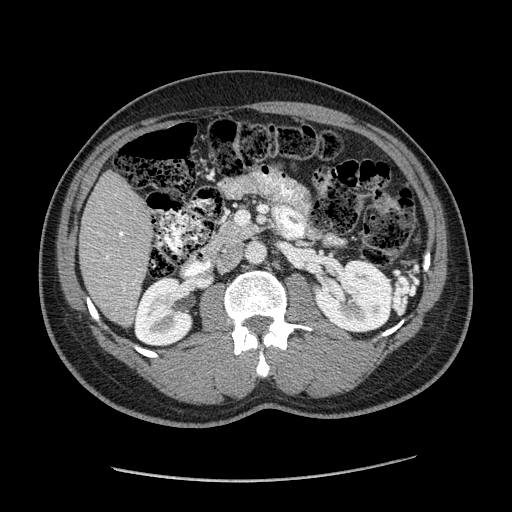
Contrast-enhanced abdominal CT (liver protocol), one axial slice; slice 63 of 182 in the series (ordered by position); 120 kVp; soft-tissue window (W 400 / L 40 HU); 512 × 512 image matrix, field of view 400 × 400 mm. Case-level facts recorded for this patient, not image findings: diagnosis: hepatocellular carcinoma (patient treated with transarterial chemoembolisation; whether this scan precedes or follows treatment is not stated here); TNM stage (as recorded): Stage-I; Child-Pugh class: A; tumour nodularity: uninodular.
Outlined on this slice (semi-automatic segmentation, software-assisted and operator-edited):
- liver parenchyma outside the tumour (the mass and vessels are separate outlines, so this box may not span the whole liver): bounding box [x1, y1, x2, y2] px = [80, 171, 152, 324]
- liver vessels: [106, 232, 123, 259]